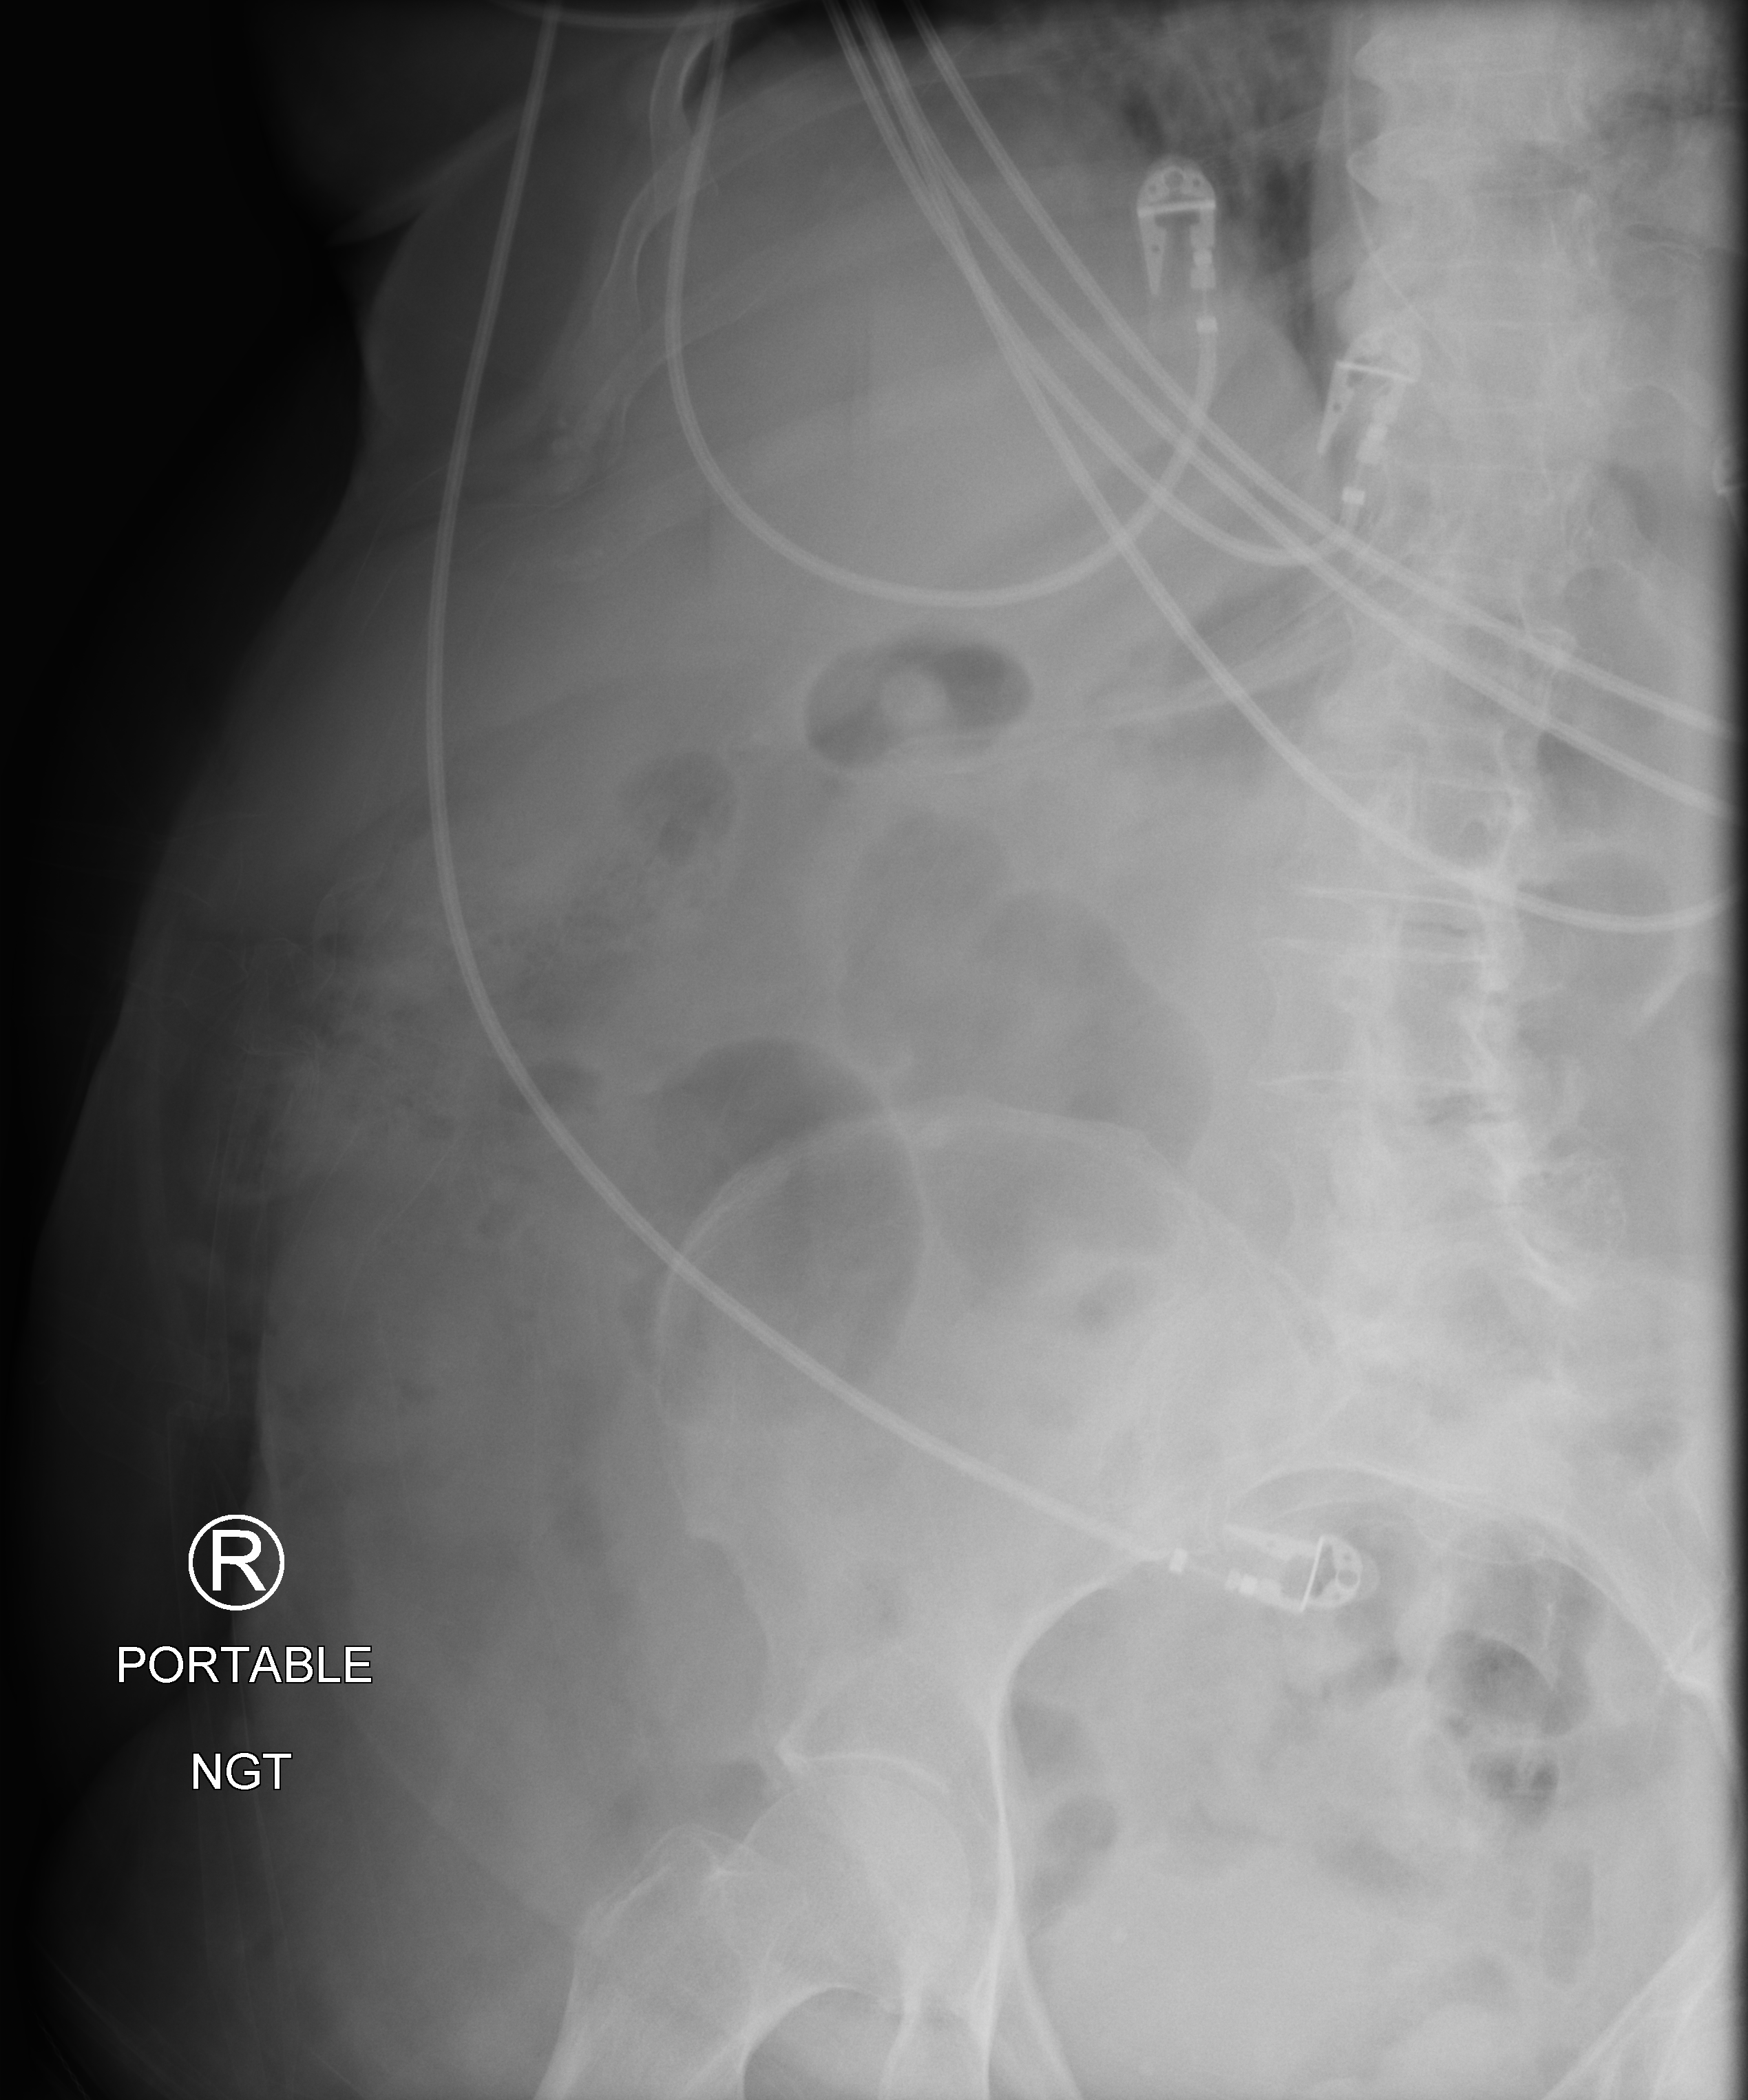
Abdomen X-ray (portable); anteroposterior (AP) projection. Patient hospitalised with COVID-19; female, aged 75–90 years.
From the hospital-stay record, not from the radiograph (when in the stay this image was taken is not recorded): mechanically ventilated during this hospital stay: yes; other chronic lung disease (admission record): yes.